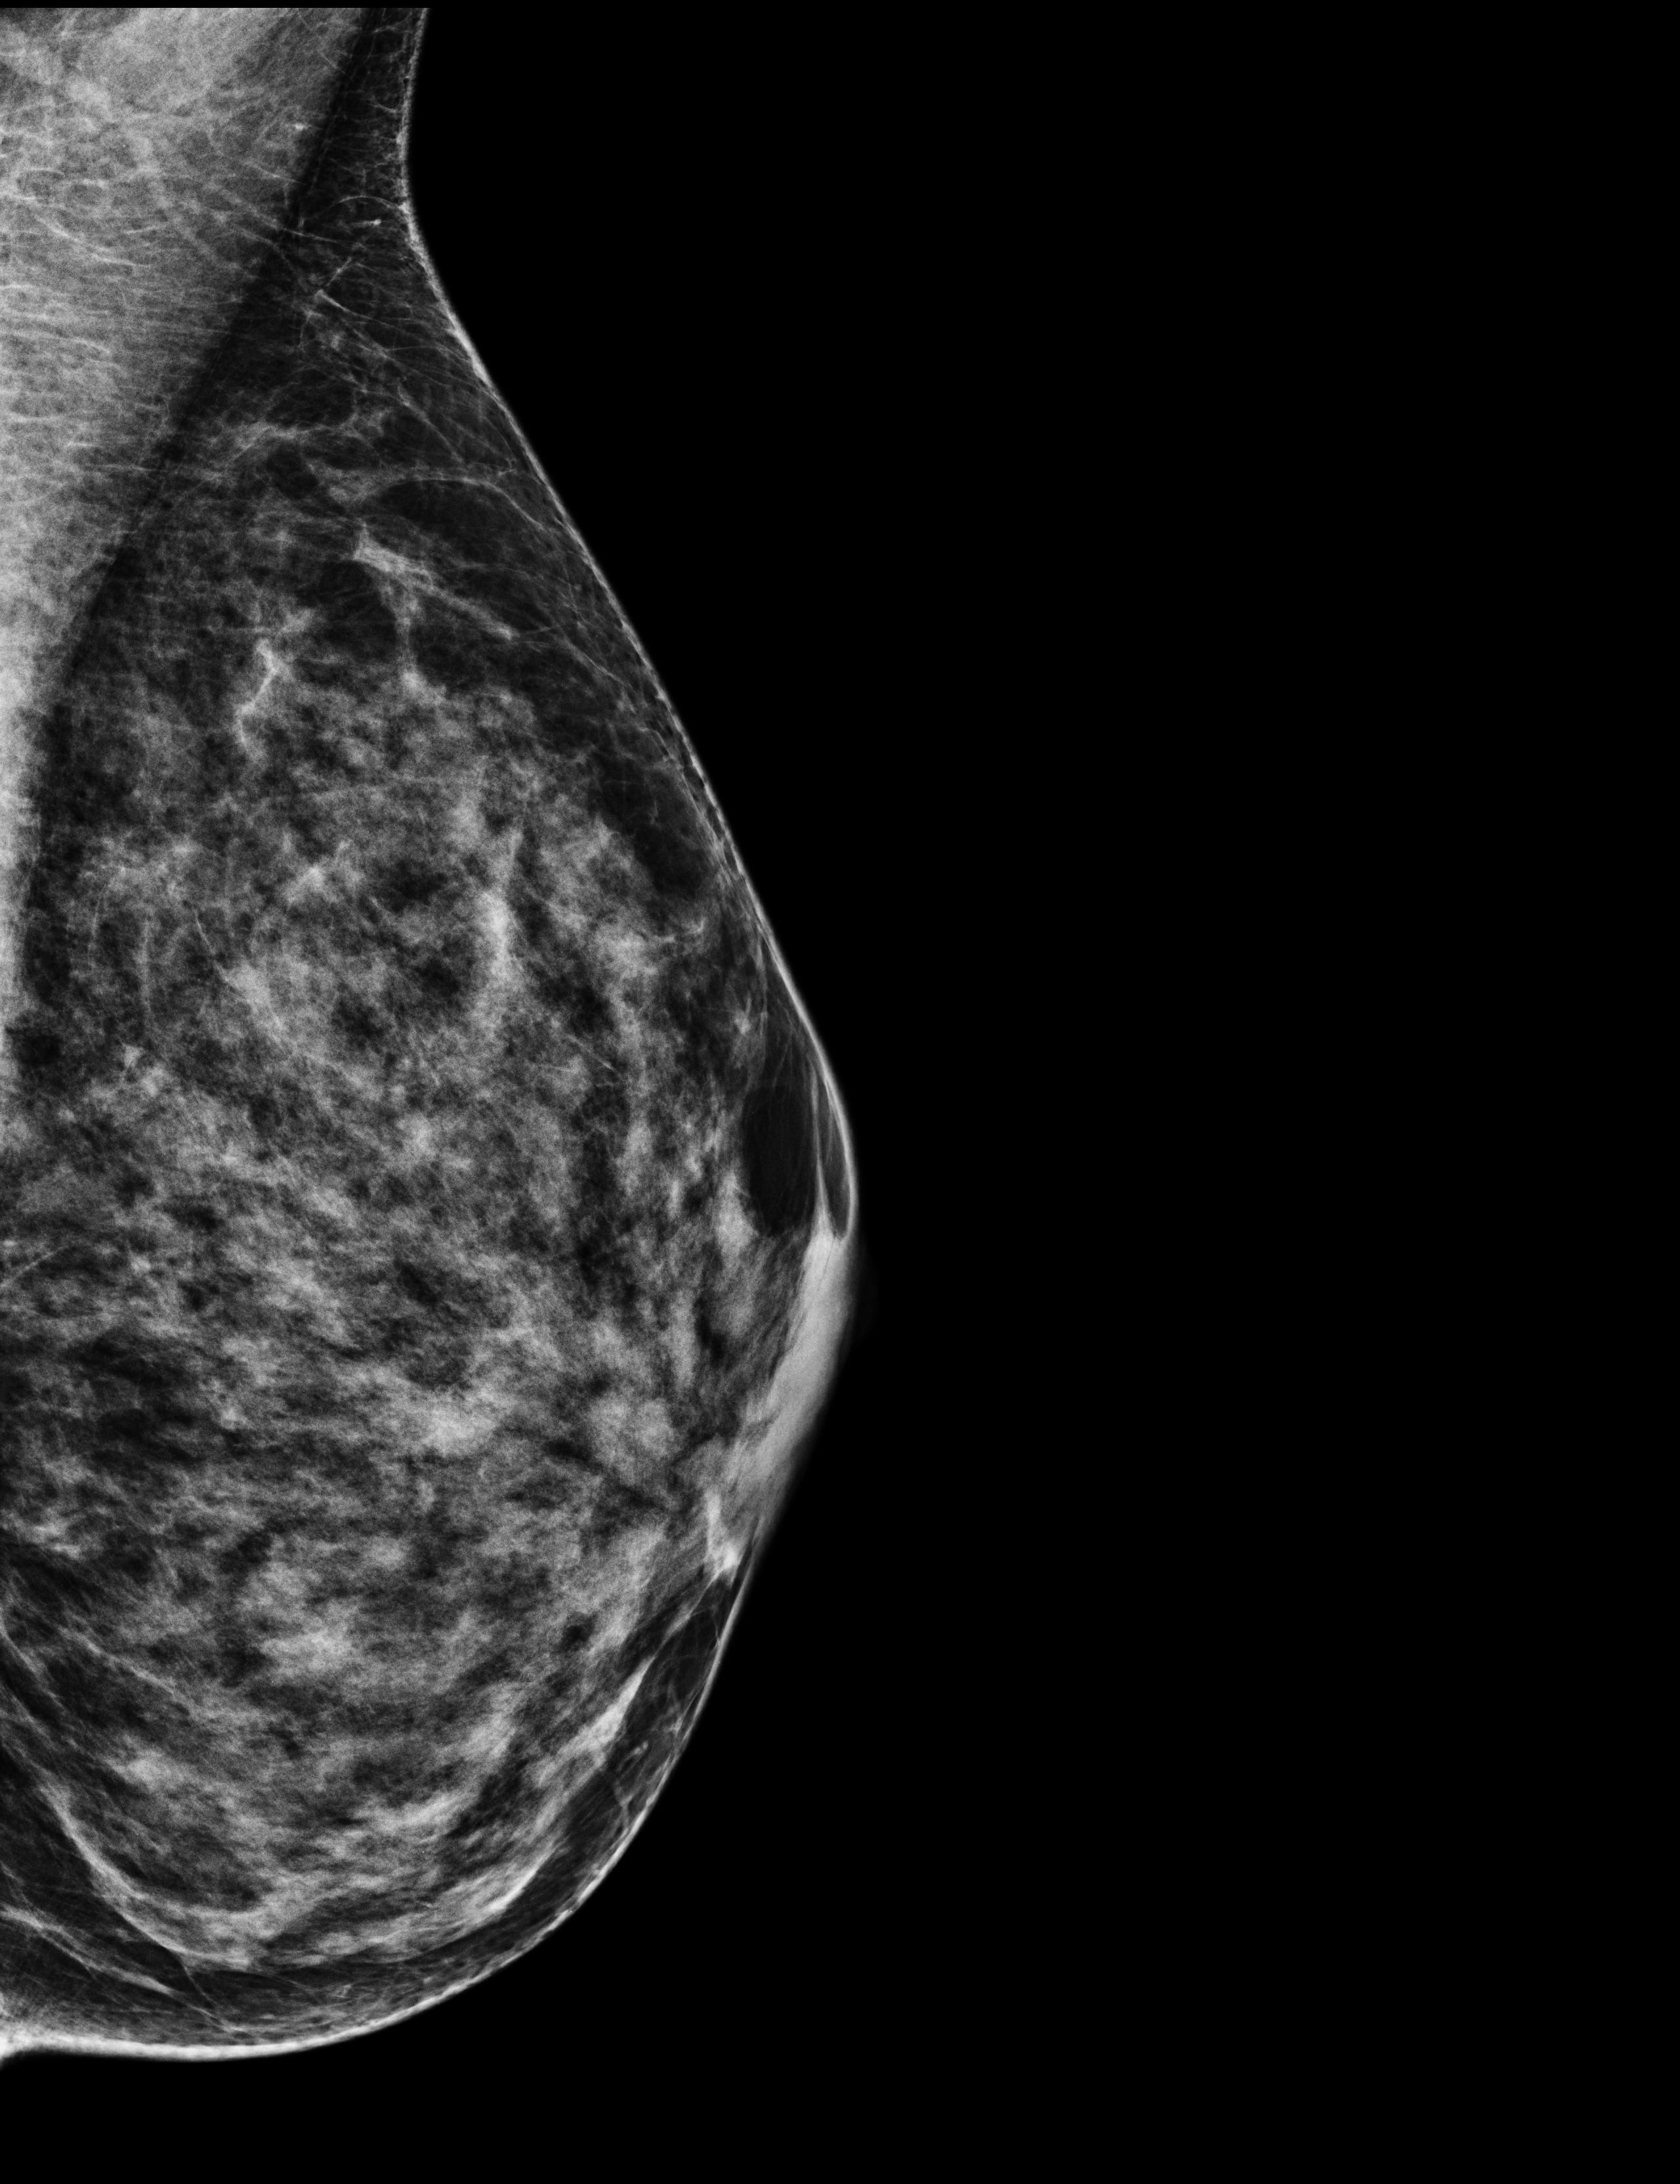
Full-field digital mammogram (FFDM); left breast; mediolateral oblique (MLO) view; screening examination; compressed breast thickness 46 mm; system: Selenia Dimensions. Patient aged 52 years (female).
BI-RADS breast density category at the screening exam (both breasts, scale 1–4): 3. Final BI-RADS category for the screening round (tomosynthesis exam, both breasts): category 2. Recall: recalled for additional imaging after this screen.